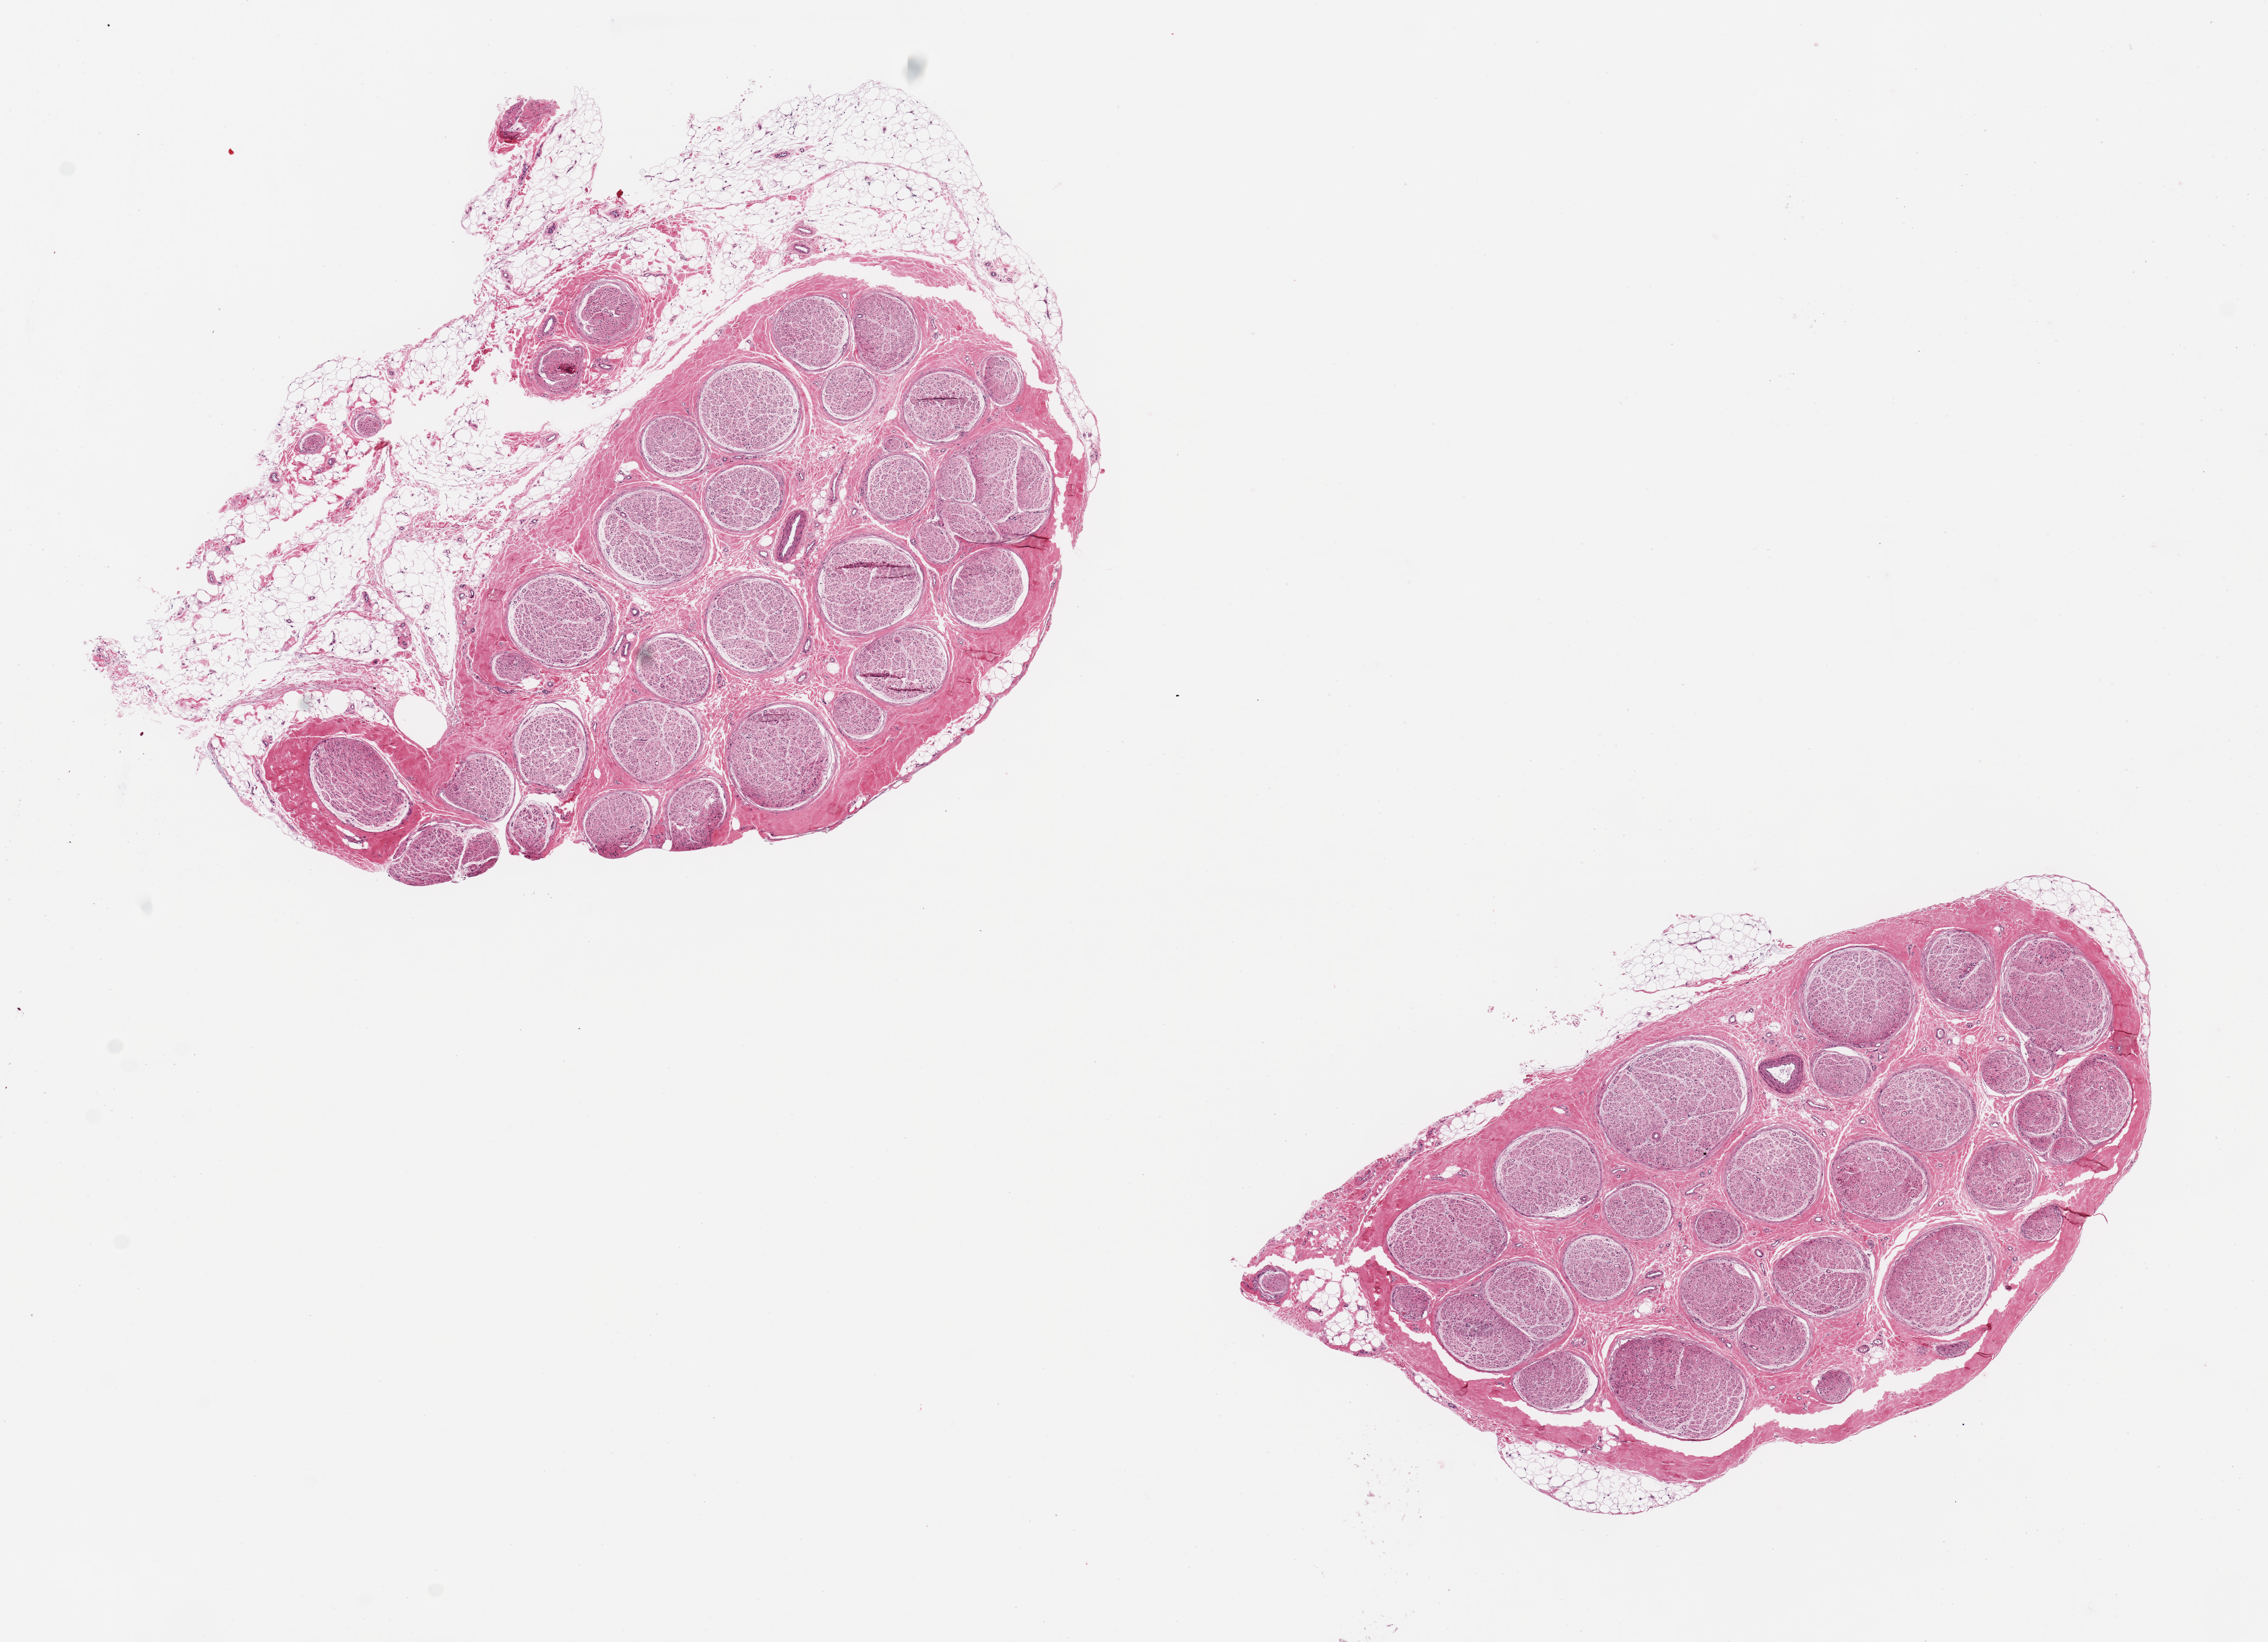
Hematoxylin and eosin (H&E) whole-slide image — low-resolution overview of the scanned area, about 14.8 x 10.7 mm (acquisition: 20x scan); PAXgene-fixed, paraffin-embedded tissue; section of tibial nerve (target tissue); donor tissue sample. Male donor.
* review note (as recorded): 2 pieces ~5x3.5mm pieces, one ~40% fat one edge